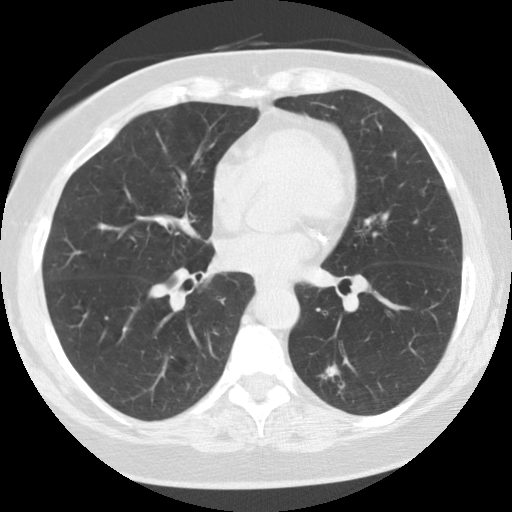
Chest CT (low-dose screening protocol), one axial image. Baseline annual screen. Lung window (W 1500 / L -600 HU). 2.5 mm slice thickness. Slice 66 of 115 in the series. Female, age 59 years at enrolment. Current smoker at enrolment.
- Expert-annotated lung lesion, bounding box (x1, y1, x2, y2) in pixels: (292, 350, 362, 415).
- The screening reader recorded 5 non-calcified nodules or masses ≥4 mm on this exam (right upper lobe, right lower lobe, left lower lobe, right lower lobe, left lower lobe); which of them this box marks is not recorded.
- Participant outcome: lung cancer diagnosed 707 days after this screen — adenocarcinoma, NOS, left lower lobe, poorly differentiated (G3), stage IA (AJCC 6th edition), 15 mm at pathology.